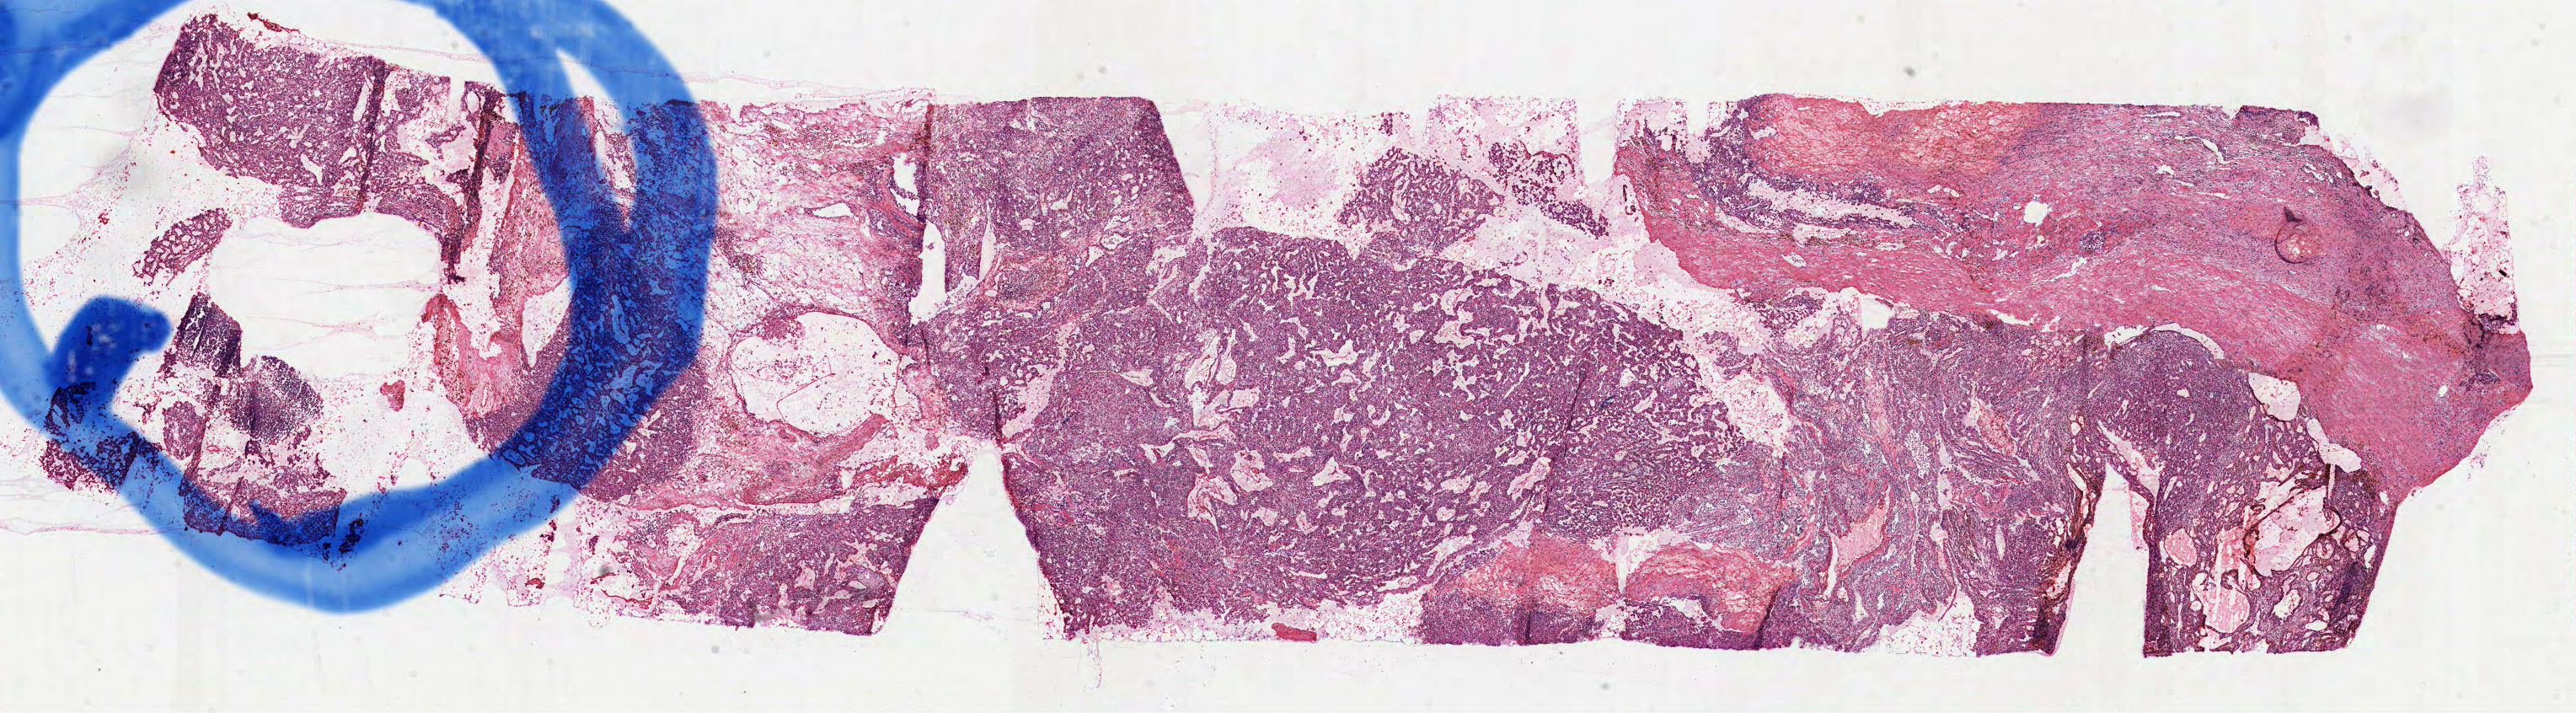
Digitized H&E-stained tissue section (whole slide), low-resolution overview of the scanned area, about 24.7 x 6.8 mm (from a 40x scan). Frozen section. Sample: primary tumour, kidney. Male, age 65 years at initial diagnosis. Histologic grade: G3 (poorly differentiated). Pathologist review of this section (percent, as recorded): tumour cells 80%, tumour nuclei 80%, normal cells 0%, stromal cells 20%, necrosis 0%.
AJCC pathologic stage: I (6th edition). TNM: T1a N0 M0. Laterality: left. Pathologic diagnosis: Clear cell adenocarcinoma, NOS.